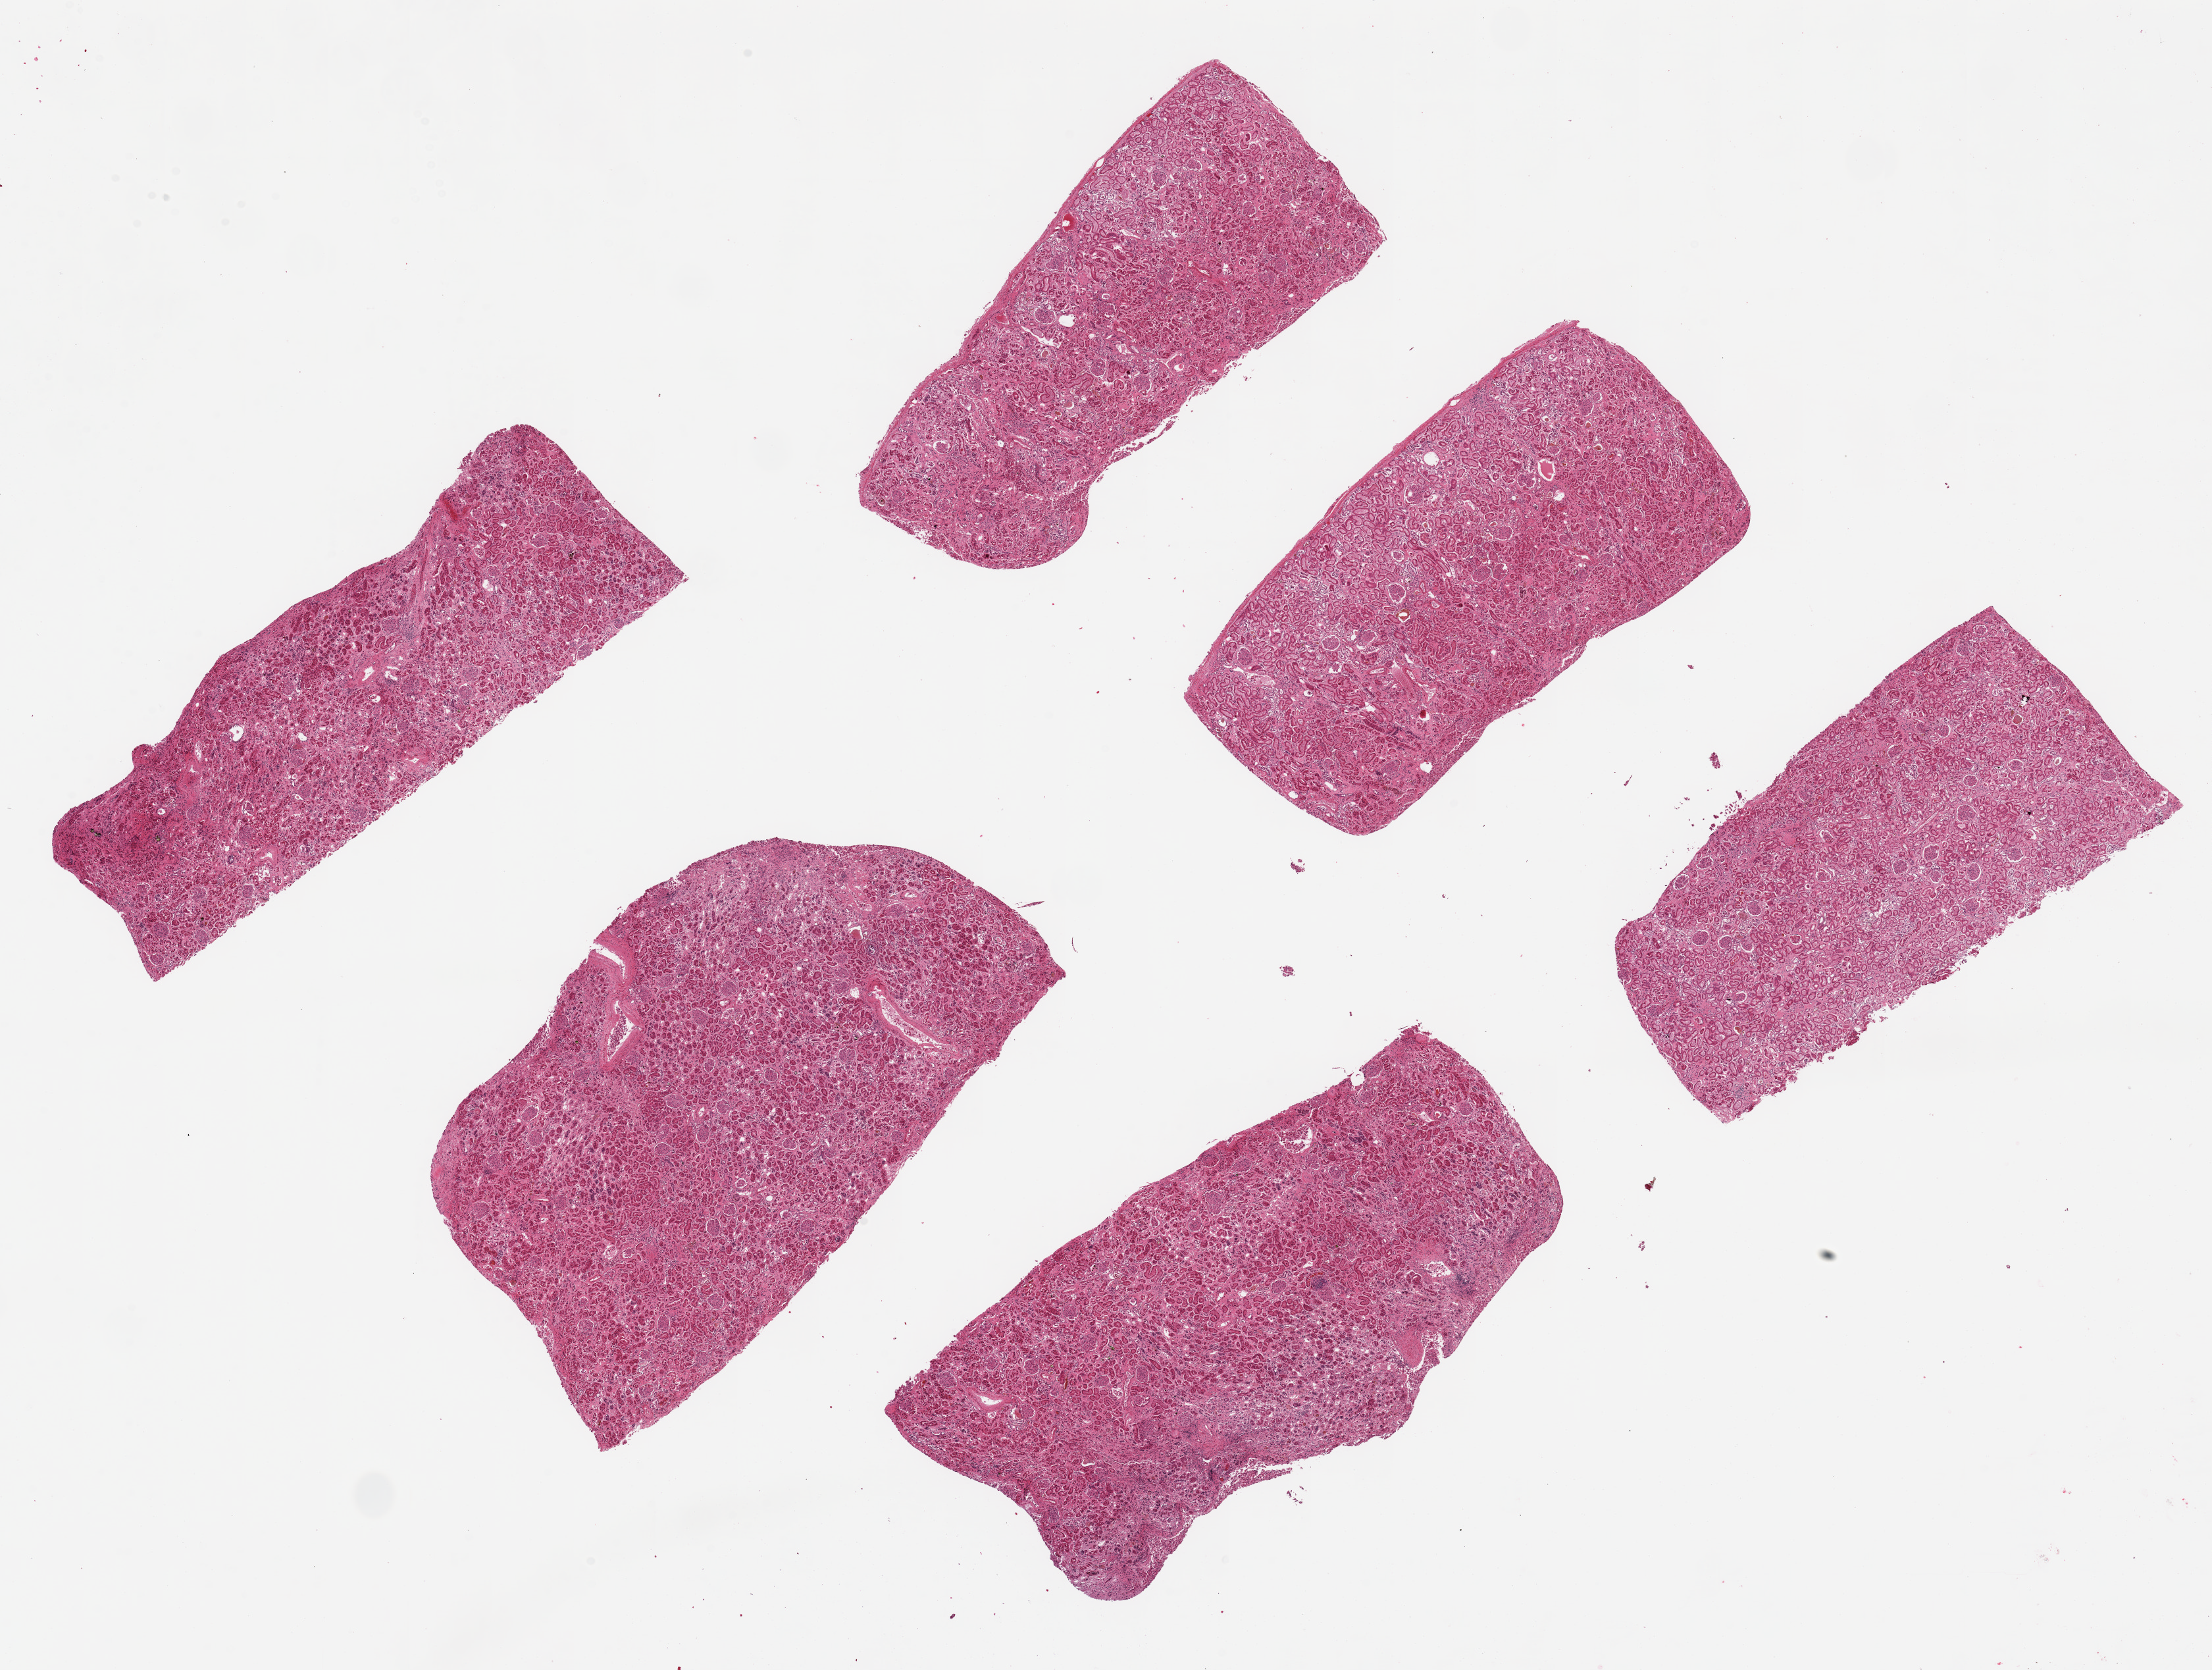
Digitized hematoxylin and eosin (H&E)-stained section — a low-resolution overview of the entire scanned area, about 26.6 x 20.1 mm. PAXgene-fixed, paraffin-embedded tissue. Sampled site (target tissue): renal cortex. Tissue donor sample. Male donor.
- reviewer comment on this tissue sample: 6 7x3.5mm pieces, tubules badly autolyzed